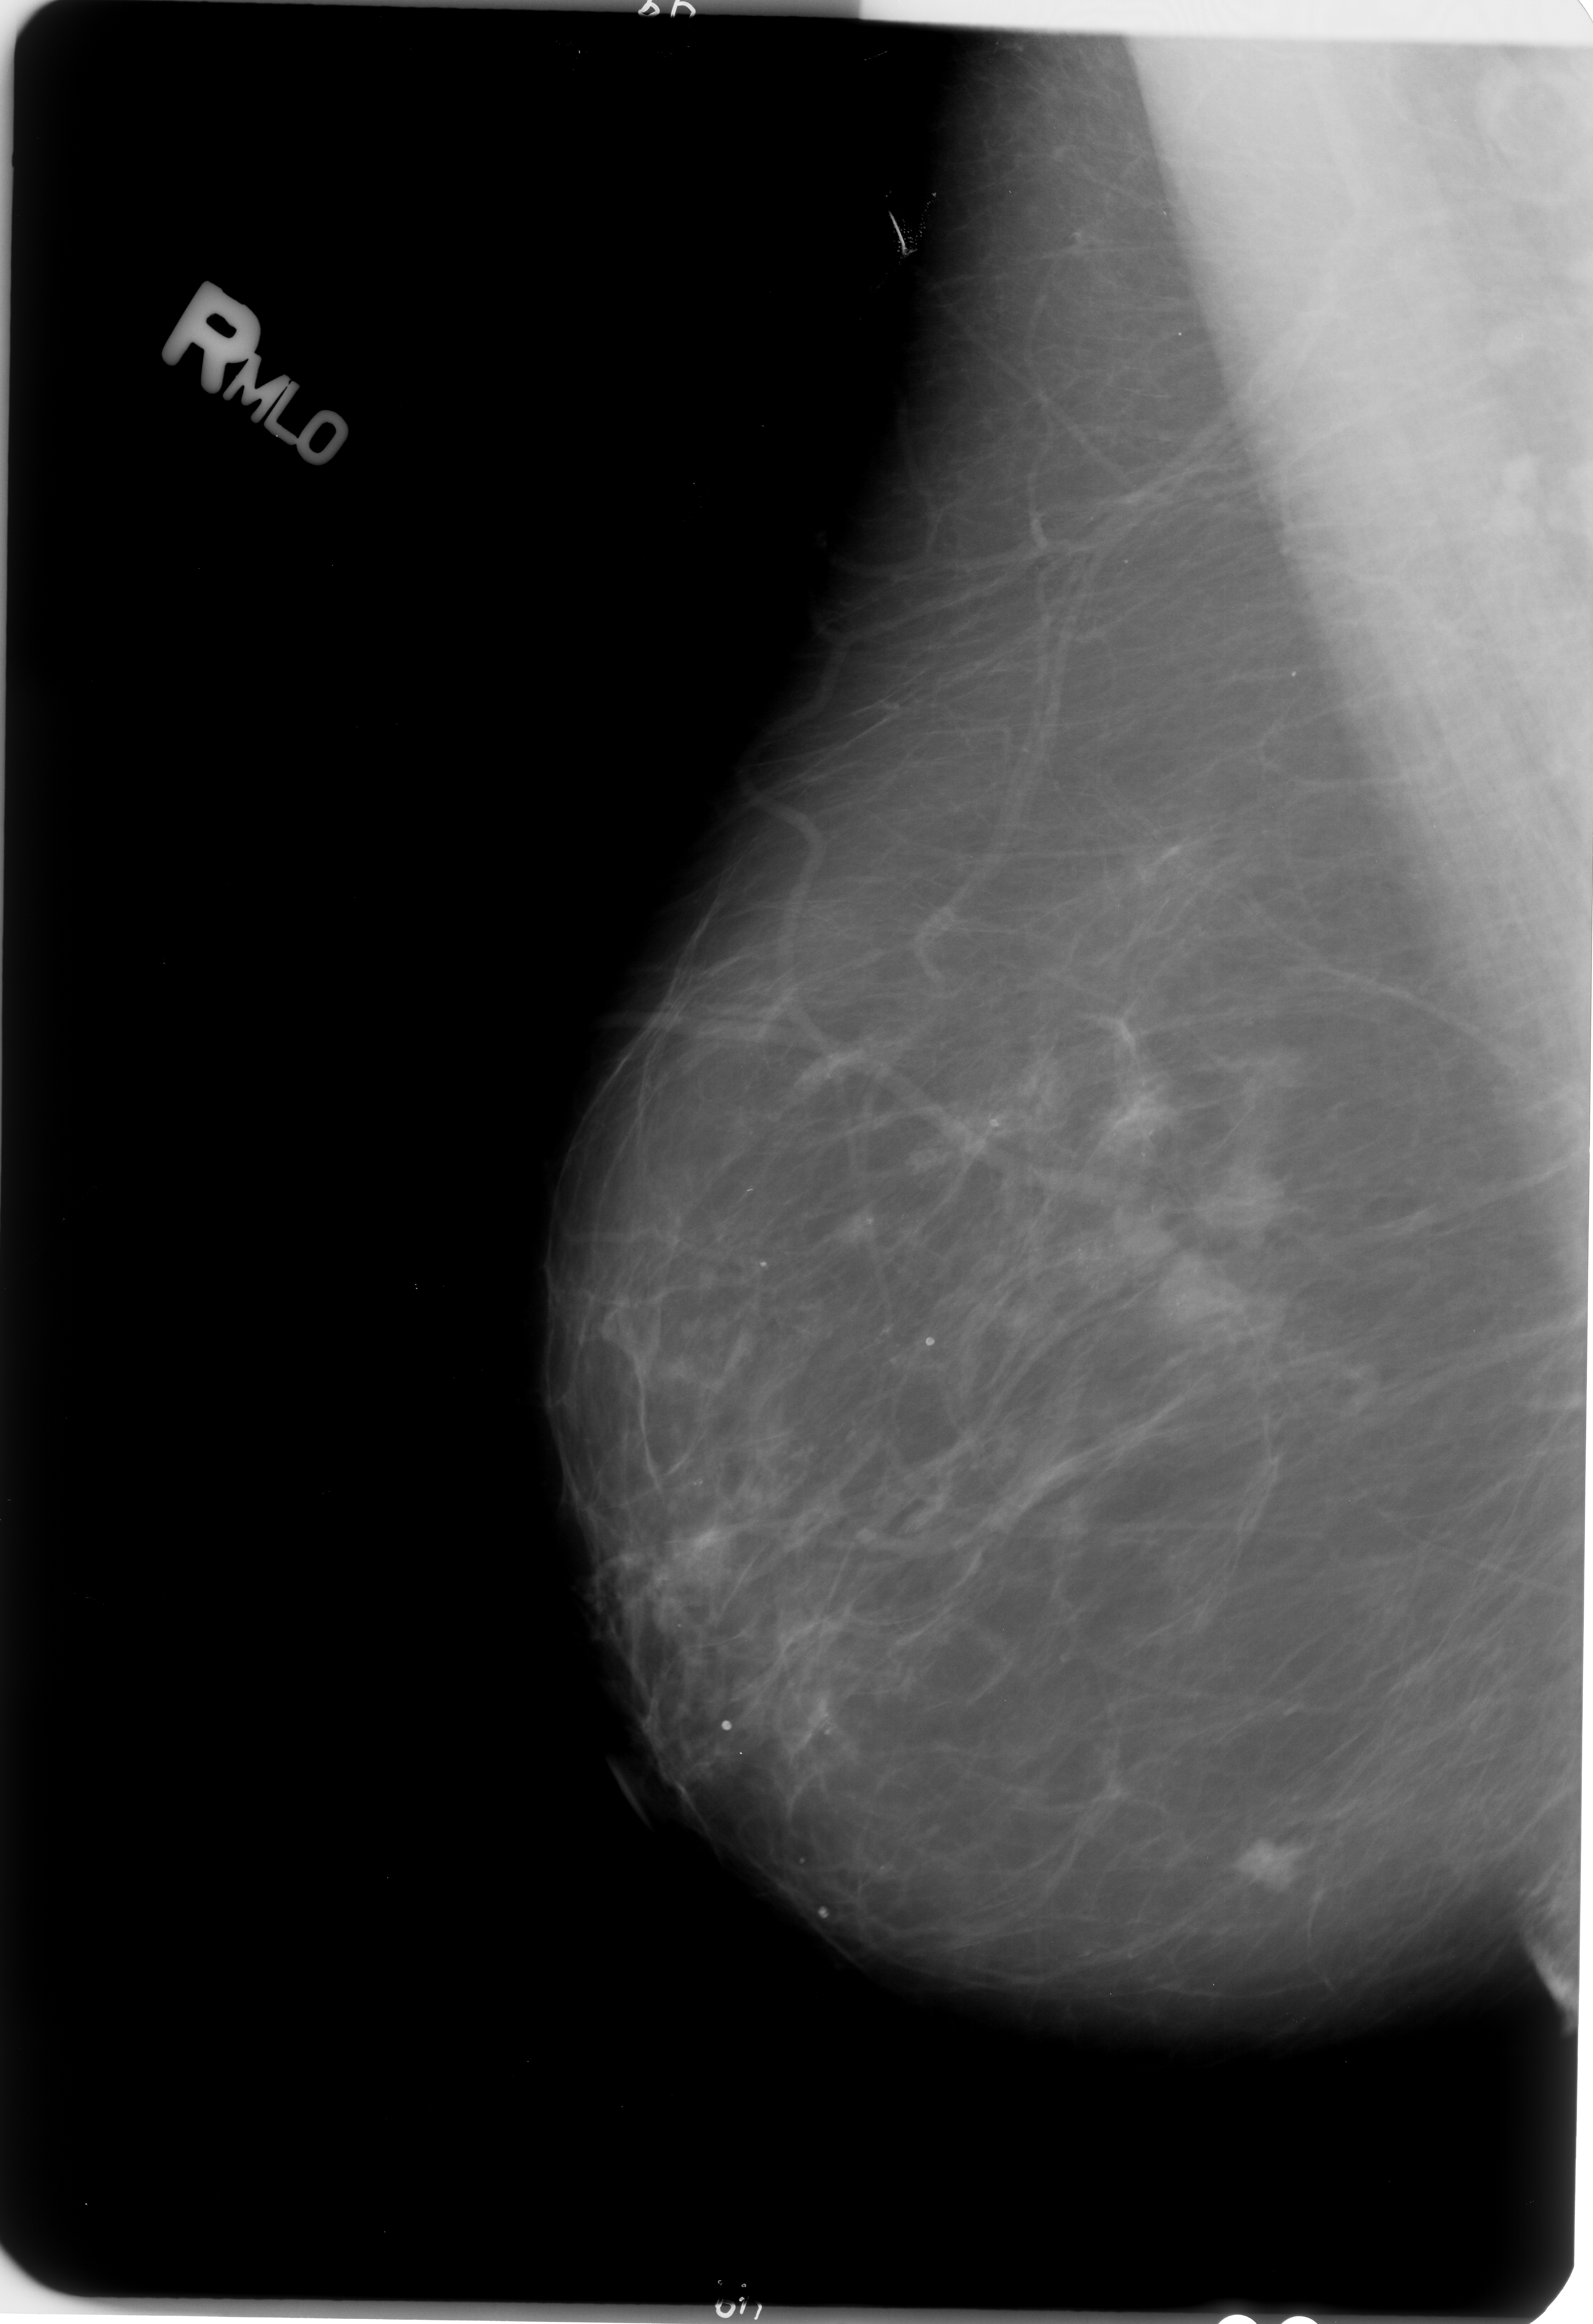
Mammogram (digitized film); right breast; MLO view; BI-RADS breast density category 2 (scale 1–4).
Abnormality record for this image: mass, shape irregular, margins microlobulated / spiculated; BI-RADS assessment category 4; pathology (as recorded): malignant.